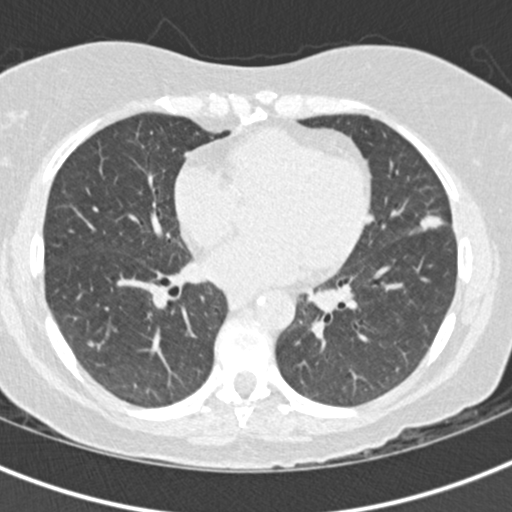
Low-dose screening chest CT, one axial slice. Slice 78 of 156 in the series (ordered by position). Lung window (W 1500 / L -600 HU). 2 mm slice thickness. 512 × 512 image matrix, field of view 298 × 298 mm.
Structures marked on this image (expert manual segmentation):
- lesion 1 (tumor, lingular bronchus): bounding box (x1, y1, x2, y2) in pixels: (421, 216, 443, 230)